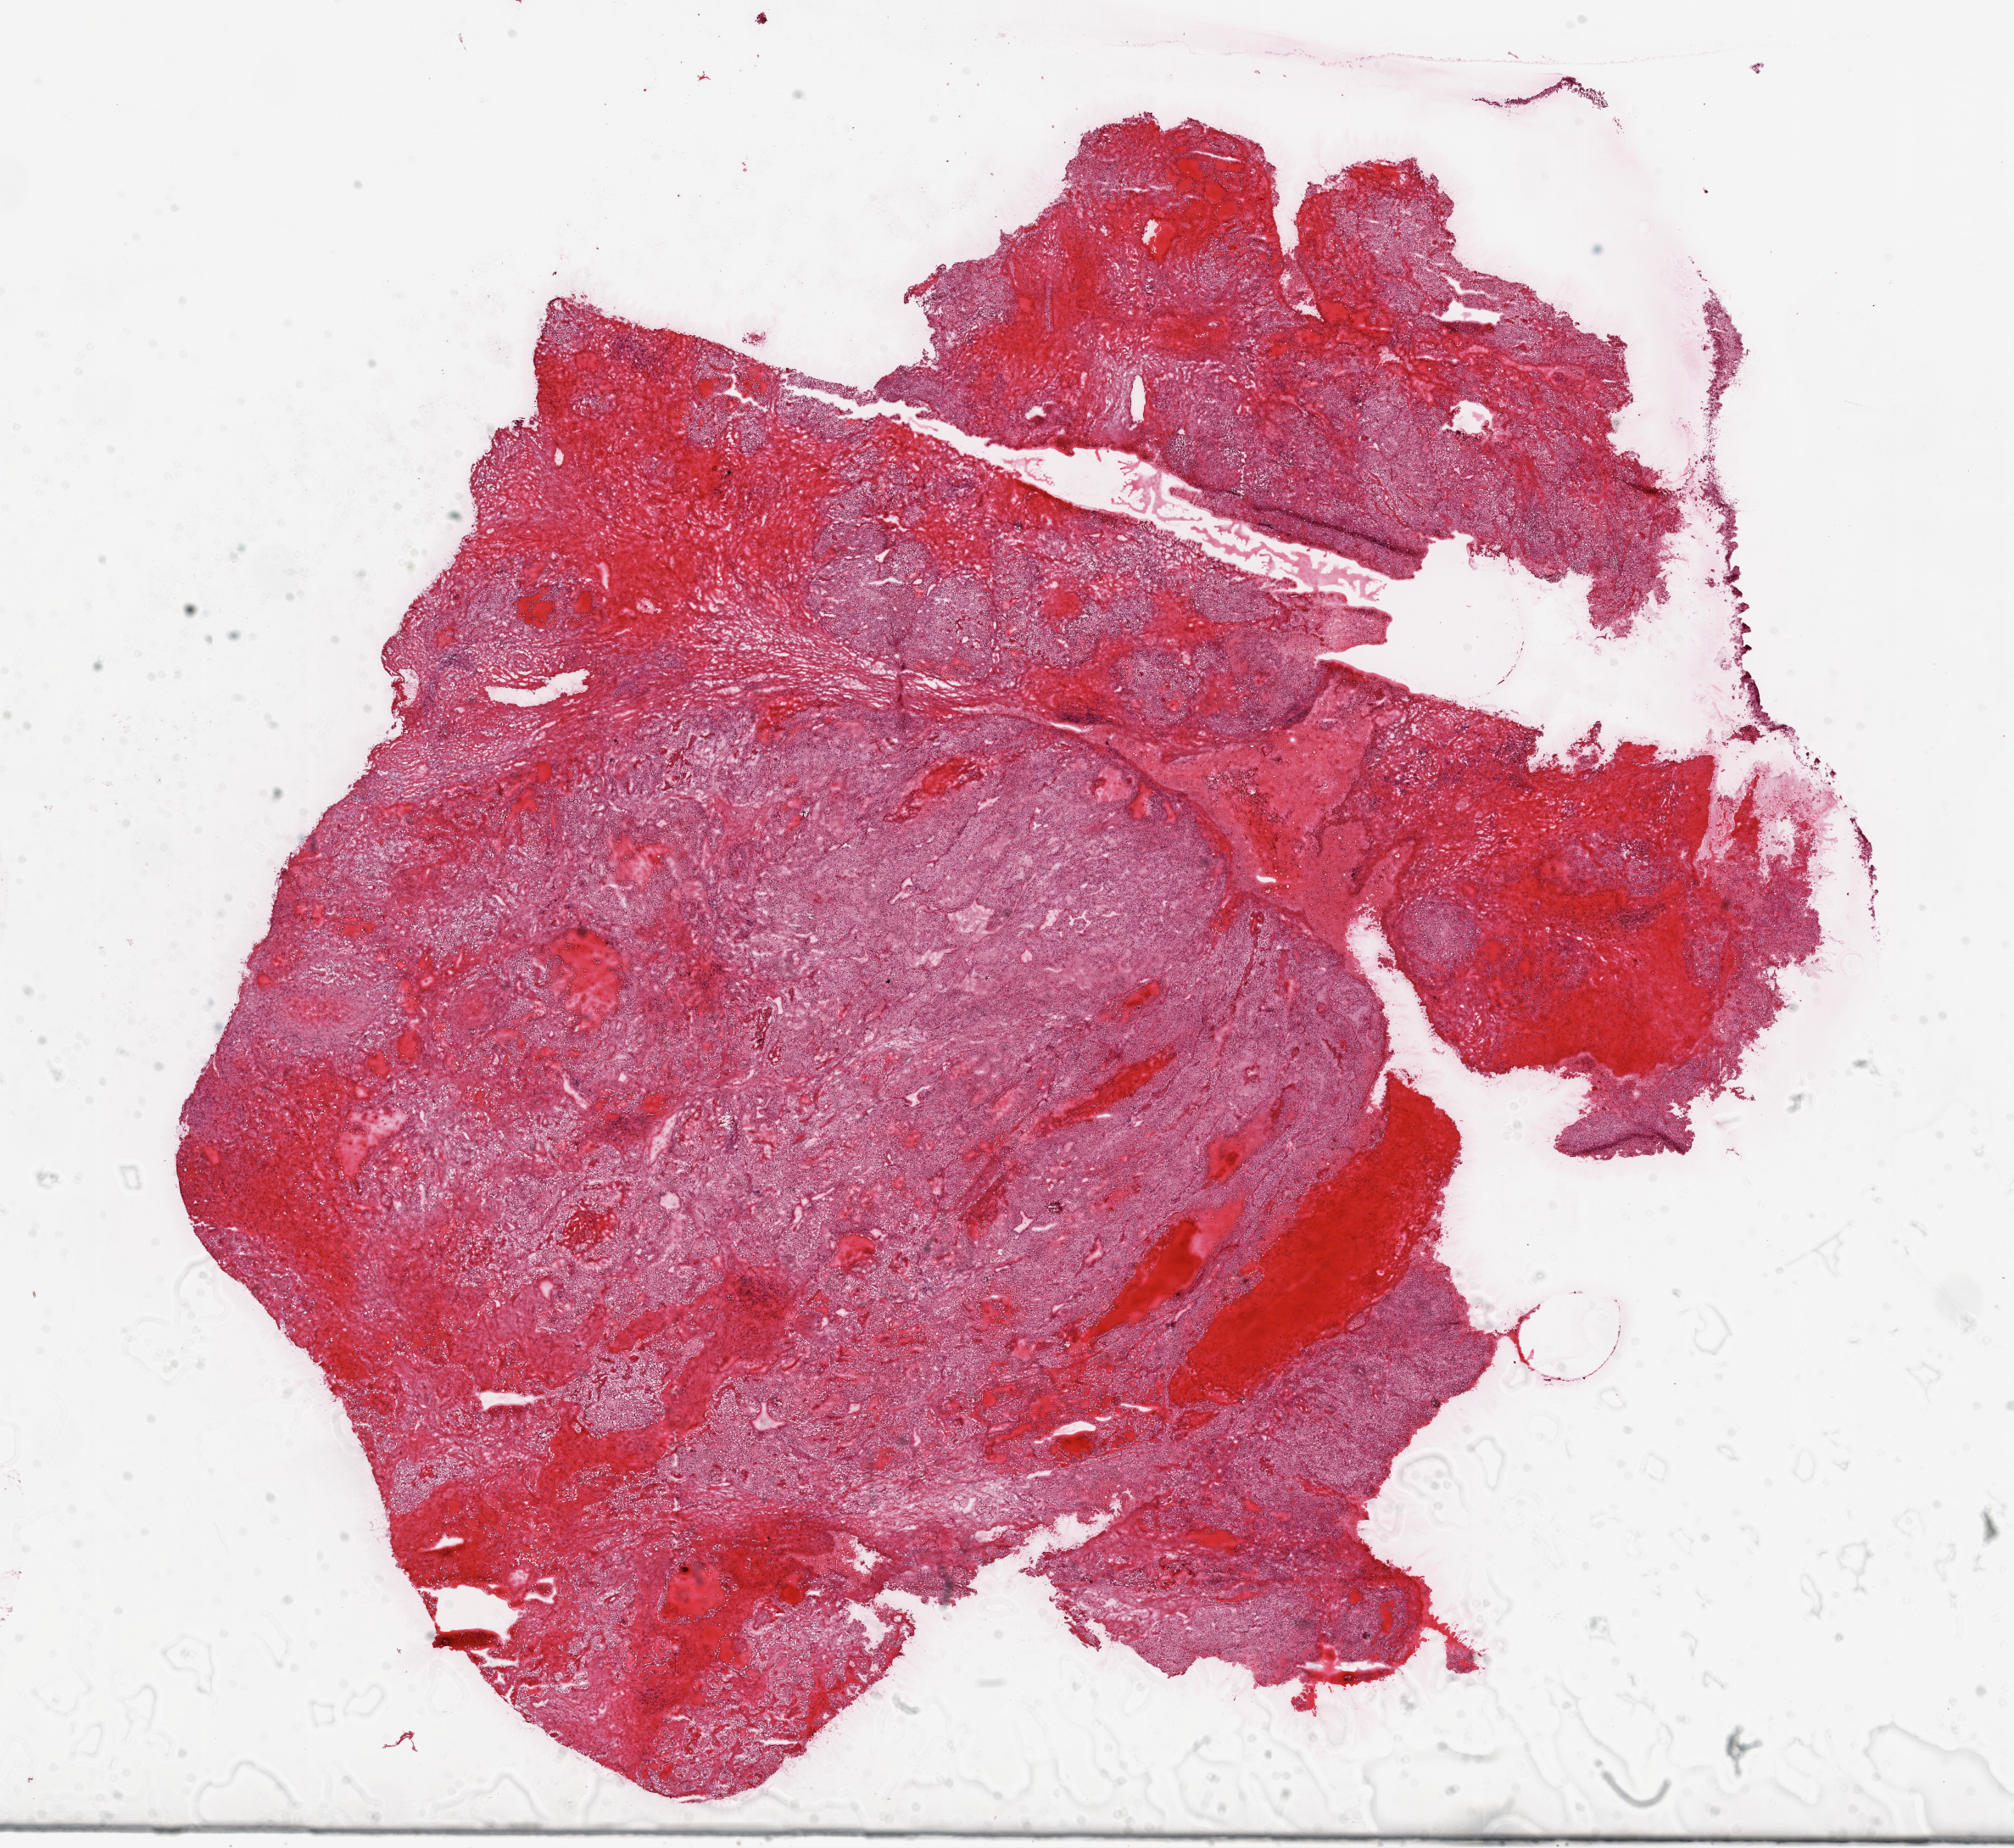
Digitized Hematoxylin and eosin (H&E) stained tissue section (whole slide) — low-resolution overview of the scanned area, about 19.1 x 17.5 mm. Frozen section. Primary tumour sample from the kidney. Patient: male, age at initial diagnosis 58 years. Histologic grade: G3 (poorly differentiated). Slide review estimates, as recorded: tumour cells 90%, tumour nuclei 85%, normal cells 0%, stromal cells 10%, necrosis 0%.
• histologic diagnosis: Clear cell adenocarcinoma, NOS
• AJCC pathologic stage: III
• lymph nodes positive (case pathology): 0 of 10 examined